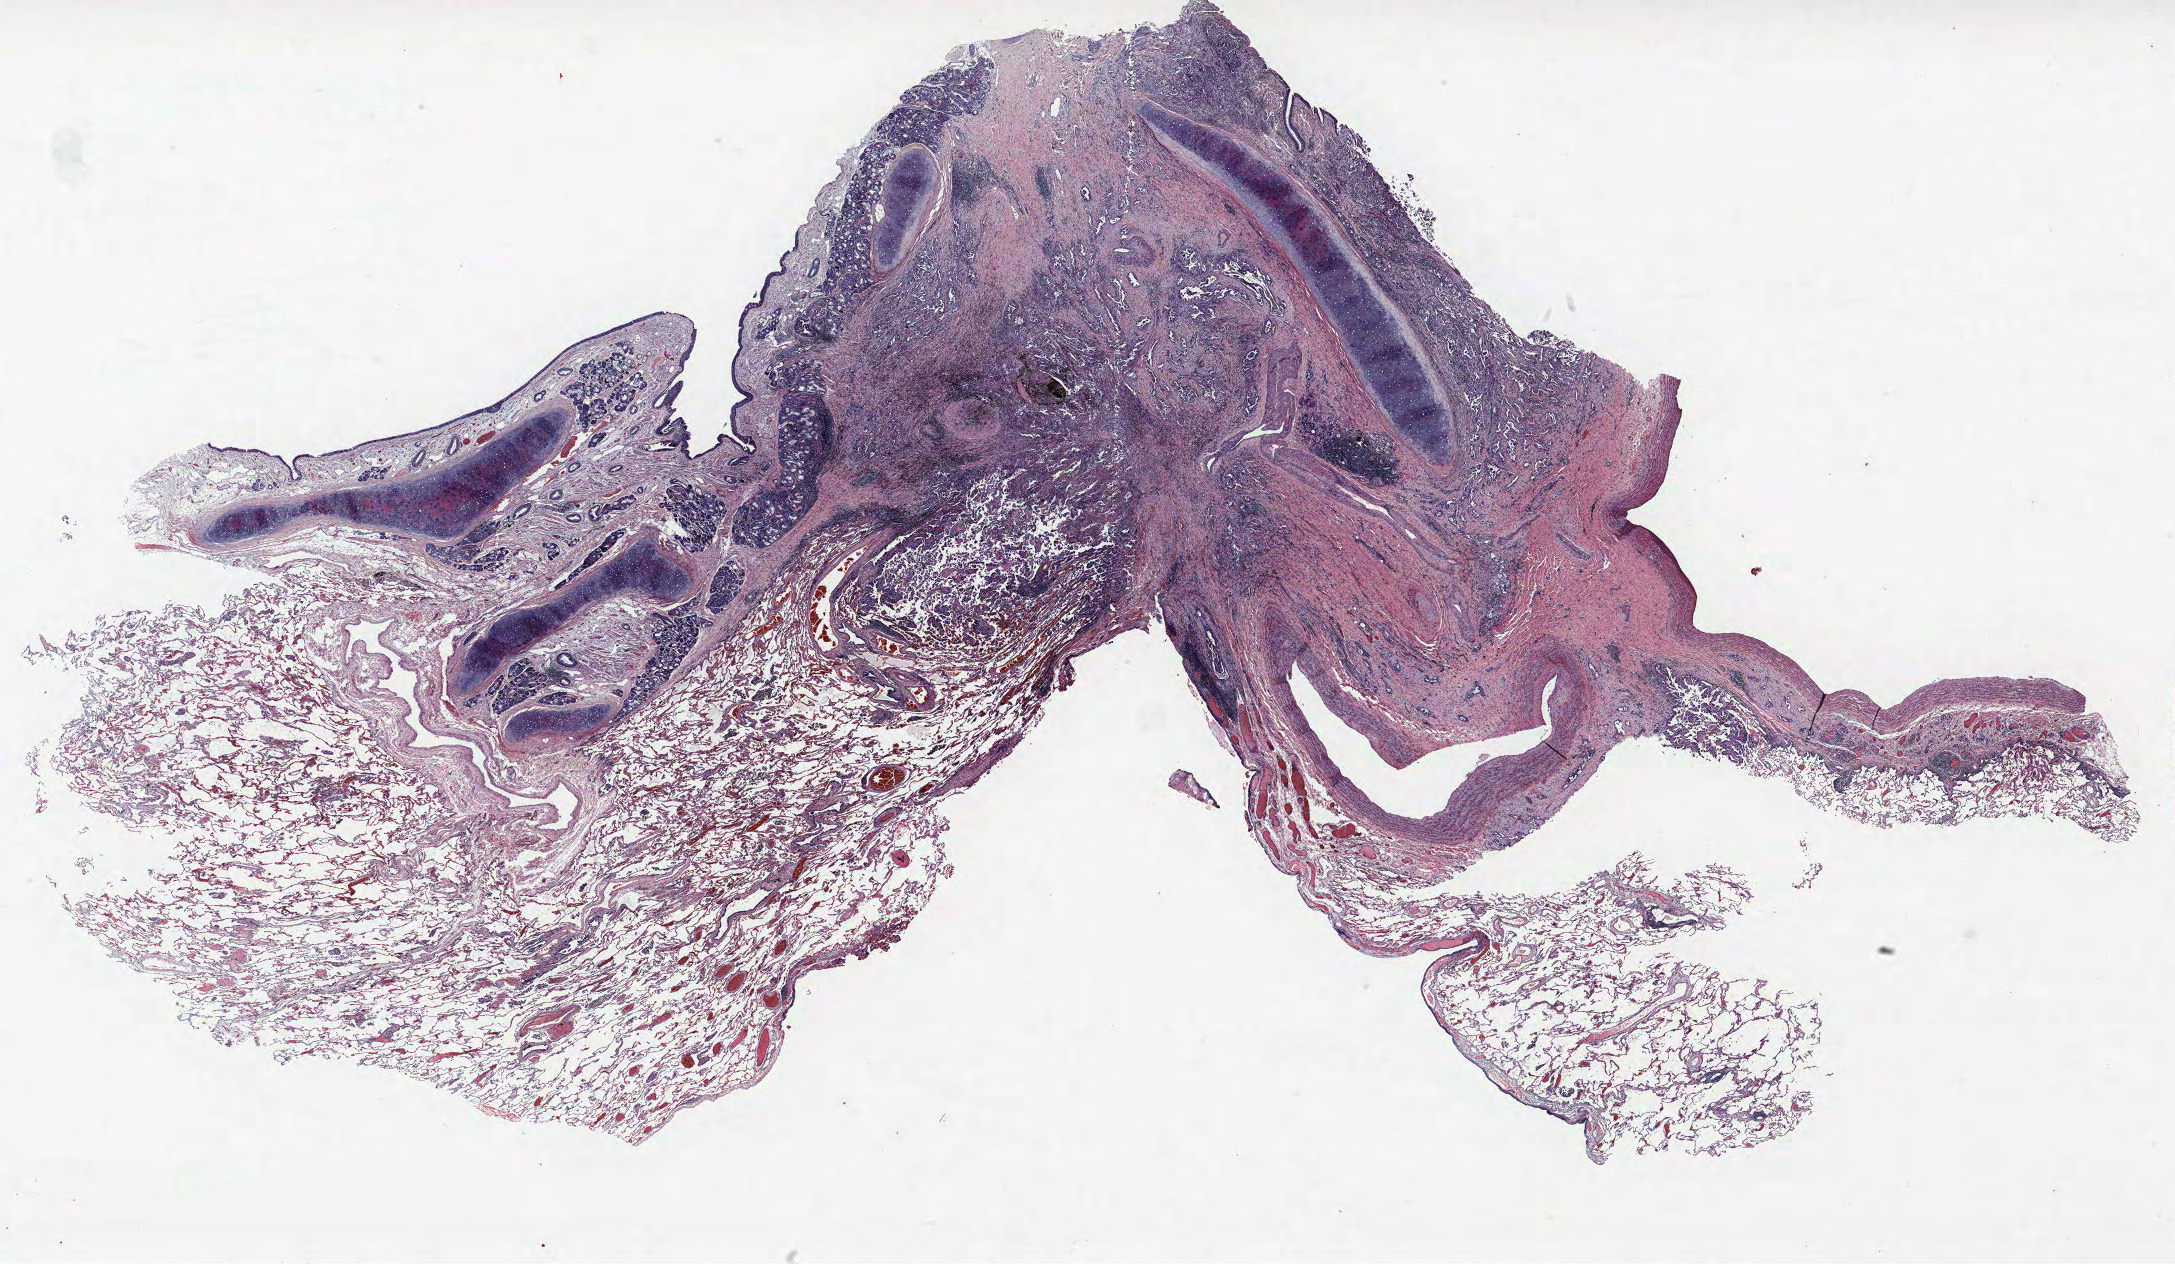
Hematoxylin and eosin (H&E) stained whole-slide image, whole scanned area (about 34.8 x 20.2 mm, from a 40x scan) shown as a low-resolution overview; FFPE section; lung. Female patient, aged 60 at enrolment. Current smoker at enrolment. Grade: moderately differentiated (G2).
• tumour size (pathology): 28 mm
• participant's lung-cancer diagnosis: Adenocarcinoma, NOS (ICD-O-3 8140/3)
• stage (AJCC 6th edition): IIIB
• primary tumour location (clinical record): right lower lobe